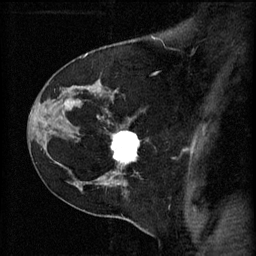
Breast MRI (dynamic contrast-enhanced), one sagittal slice; slice 42 of 60 in the series (ordered by position); 3 images stored at this slice position (order not interpretable as contrast timing); 1.5 T; TE 4.2 ms, TR 11 ms; 2 mm slice thickness; 256 × 256 image matrix, field of view 180 × 180 mm. Female patient, age 45 years.
Structures marked on this image (semi-automatic segmentation, software-assisted and operator-edited):
- analysis volume of interest (the breast-tissue region the enhancement analysis was run in; not a lesion): box from (x=110, y=128) to (x=143, y=171) px
- tumour enhancement mask (voxels above the 70 % enhancement threshold inside the analysis volume of interest): (x=112, y=132)–(x=141, y=165)